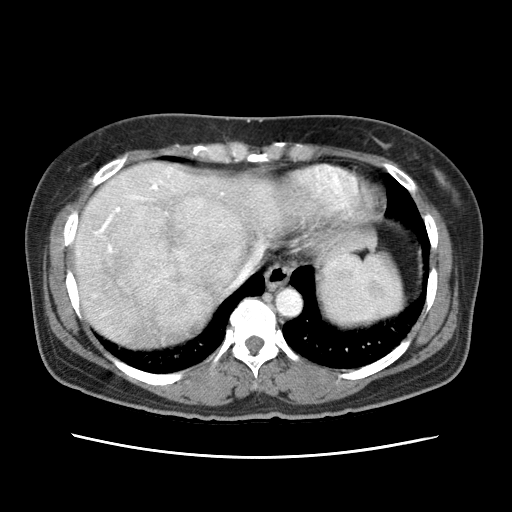
Contrast-enhanced abdominal CT (liver protocol), one axial slice; slice 58 of 79 in the series (ordered by position); 120 kVp; soft-tissue window (W 400 / L 40 HU); 2.5 mm slice thickness; 512 × 512 image matrix, field of view 340 × 340 mm. From the clinical record (not read from this slice): diagnosis: hepatocellular carcinoma (patient treated with transarterial chemoembolisation; whether this scan precedes or follows treatment is not stated here); TNM stage (as recorded): Stage-I; Child-Pugh class: A; tumour differentiation: moderately differentiated; tumour nodularity: uninodular.
Outlined on this slice (semi-automatic segmentation, software-assisted and operator-edited):
- abdominal aorta: bounding box (x1, y1, x2, y2) in pixels: (274, 288, 301, 317)
- liver parenchyma outside the tumour (the mass and vessels are separate outlines, so this box may not span the whole liver): (74, 162, 374, 346)
- mass: (108, 193, 246, 324)
- liver vessels: (78, 168, 233, 287)